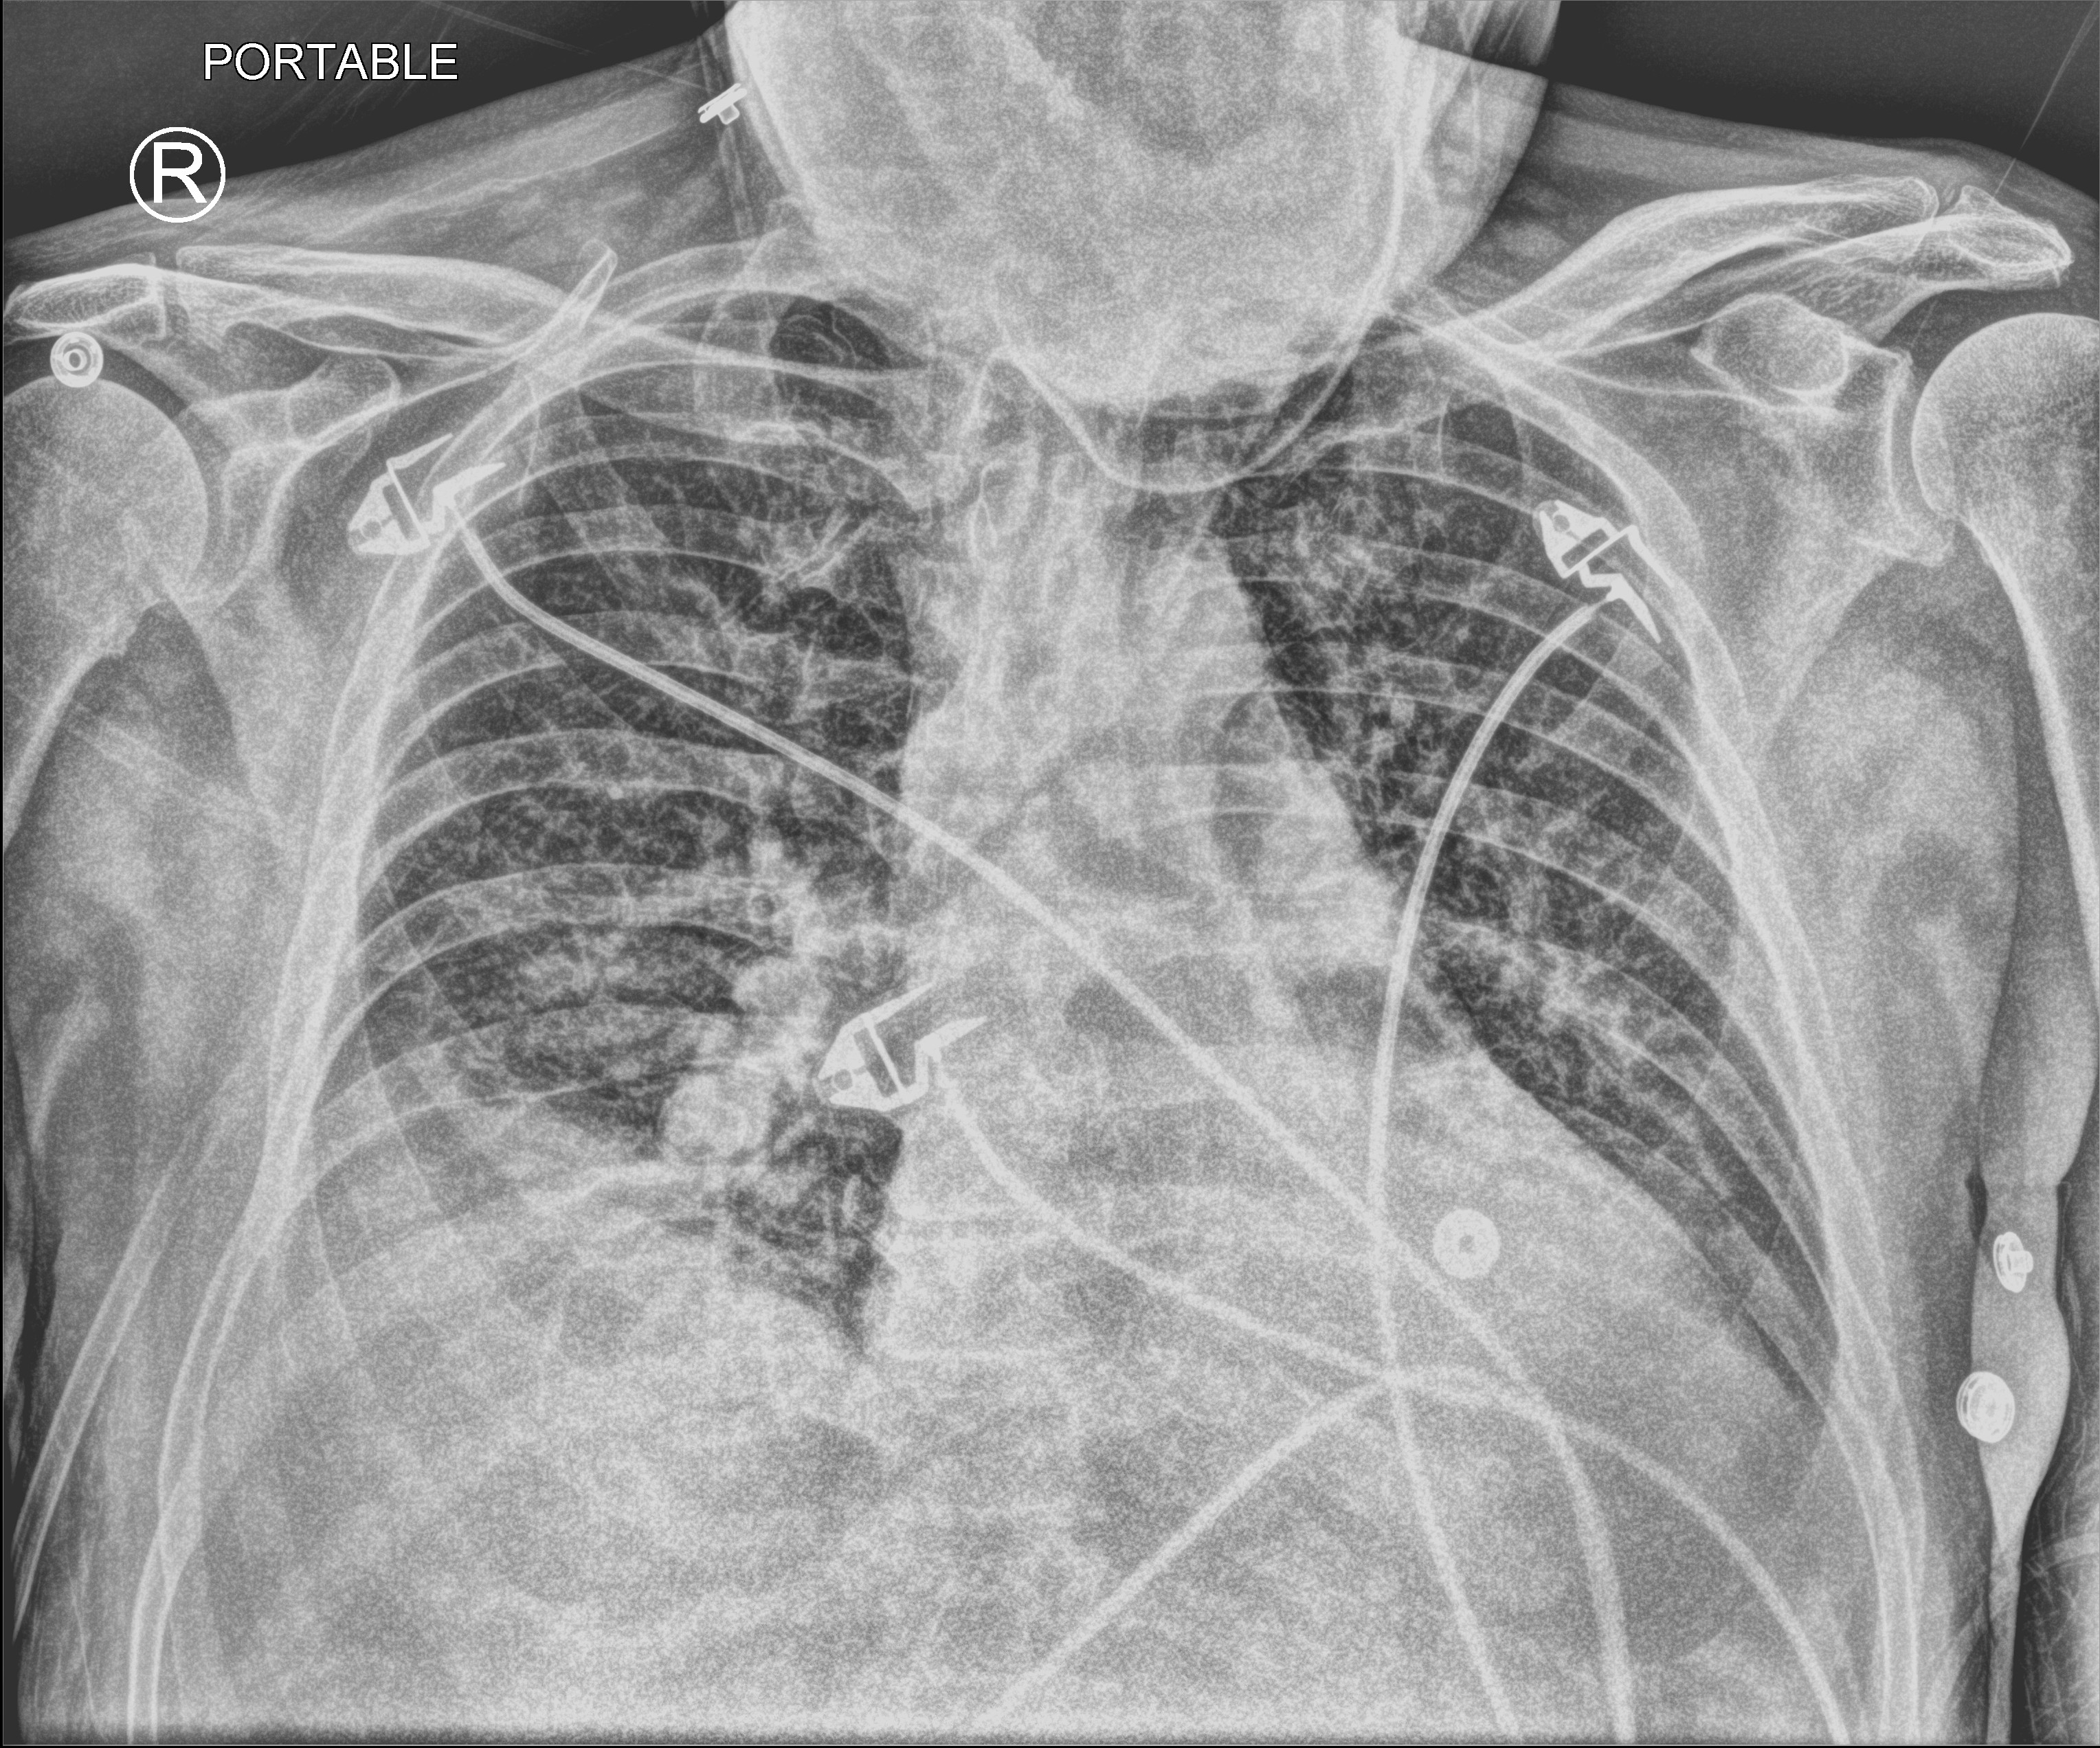
Portable chest radiograph; anteroposterior (AP) projection. Male patient hospitalised with COVID-19, age 18–59 years.
Hospital-stay facts (about this admission, not read from this image; timing relative to this image not recorded):
- admitted to intensive care during this hospital stay: no
- mechanically ventilated during this hospital stay: no